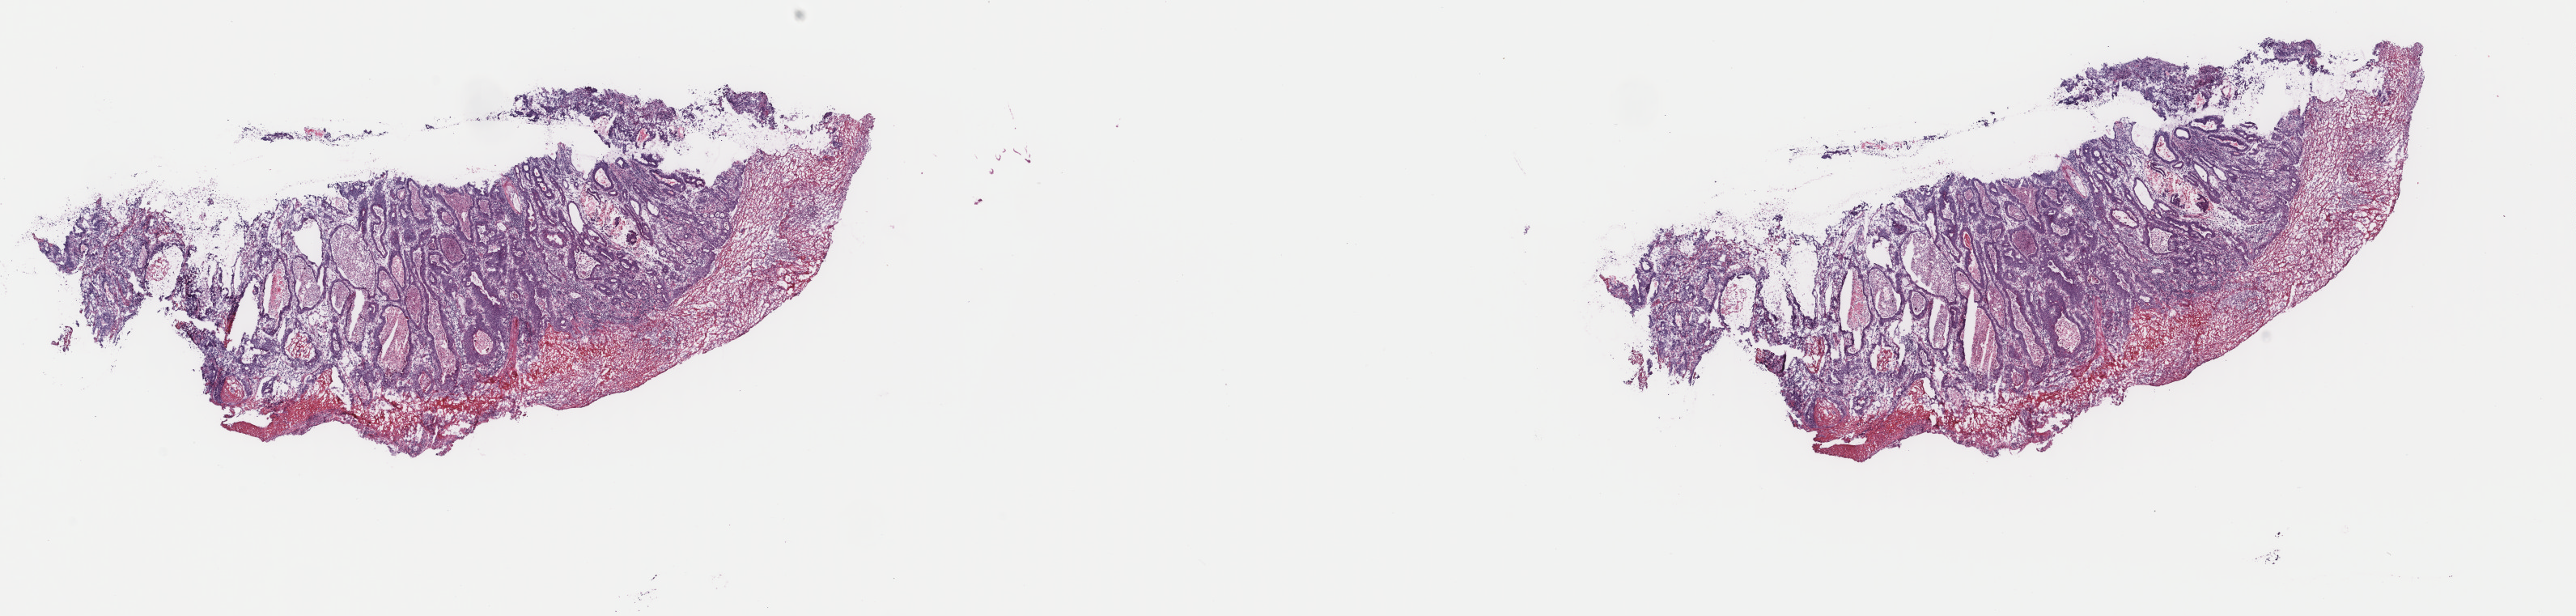
Whole-slide histology image, H&E, low-resolution overview of the scanned area, about 25.3 x 6.0 mm. Frozen section from the top of the tissue portion. Stomach, primary tumour sample. Male patient; age at initial diagnosis 76 years. Histologic grade: G2 (moderately differentiated). Pathologist review of this section (percent, as recorded): tumour cells 60%, tumour nuclei 60%, normal cells 0%, stromal cells 30%, necrosis 10%. Inflammatory infiltration, as recorded: lymphocyte infiltration 3%, monocyte infiltration 2%, neutrophil infiltration 5%.
• histologic diagnosis: Adenocarcinoma, NOS
• lymph nodes positive (case pathology): 0 of 27 examined
• AJCC pathologic stage: IA (7th edition)
• TNM: T1b N0 M0